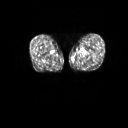
FDG PET of an extremity soft-tissue mass (from a PET/CT study), one axial slice. Slice 7 of 267 in the series (ordered by position). 128 × 128 image matrix, field of view 600 × 600 mm. Male patient, age 59 years. Case-level facts recorded for this patient, not image findings: histological type: pleiomorphic liposarcoma; grade: high; site of the primary tumour: left thigh.
Structures marked on this image (expert contour drawn on MRI and transferred to this co-registered scan by the dataset authors):
- gross tumour volume including surrounding oedema: bounding box <79,52,87,58> (left, top, right, bottom; pixels)